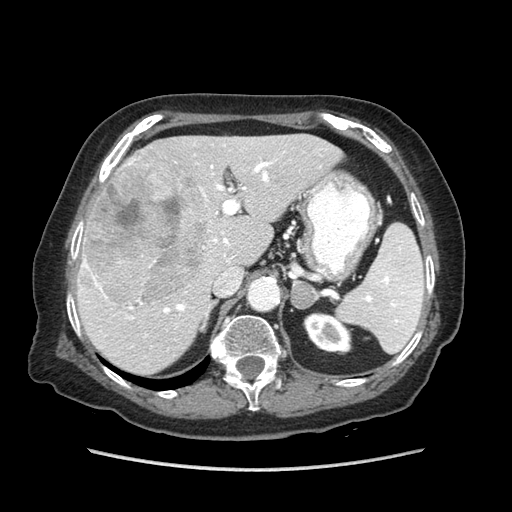
Contrast-enhanced abdominal CT (liver protocol), one axial slice. Slice 52 of 89 in the series (ordered by position). Reconstruction kernel STANDARD. 140 kVp. Soft-tissue window (W 400 / L 40 HU). 512 × 512 image matrix, field of view 360 × 360 mm. Case-level facts recorded for this patient, not image findings: diagnosis: hepatocellular carcinoma (patient treated with transarterial chemoembolisation; whether this scan precedes or follows treatment is not stated here); TNM stage (as recorded): Stage-IIIA; Child-Pugh class: A; tumour differentiation: well differentiated; tumour nodularity: multinodular.
Structures marked on this image (semi-automatic segmentation, software-assisted and operator-edited):
- liver parenchyma outside the tumour (the mass and vessels are separate outlines, so this box may not span the whole liver): bounding box (x1, y1, x2, y2) in pixels: (76, 134, 342, 374)
- mass: (84, 160, 208, 303)
- liver vessels: (82, 162, 272, 320)